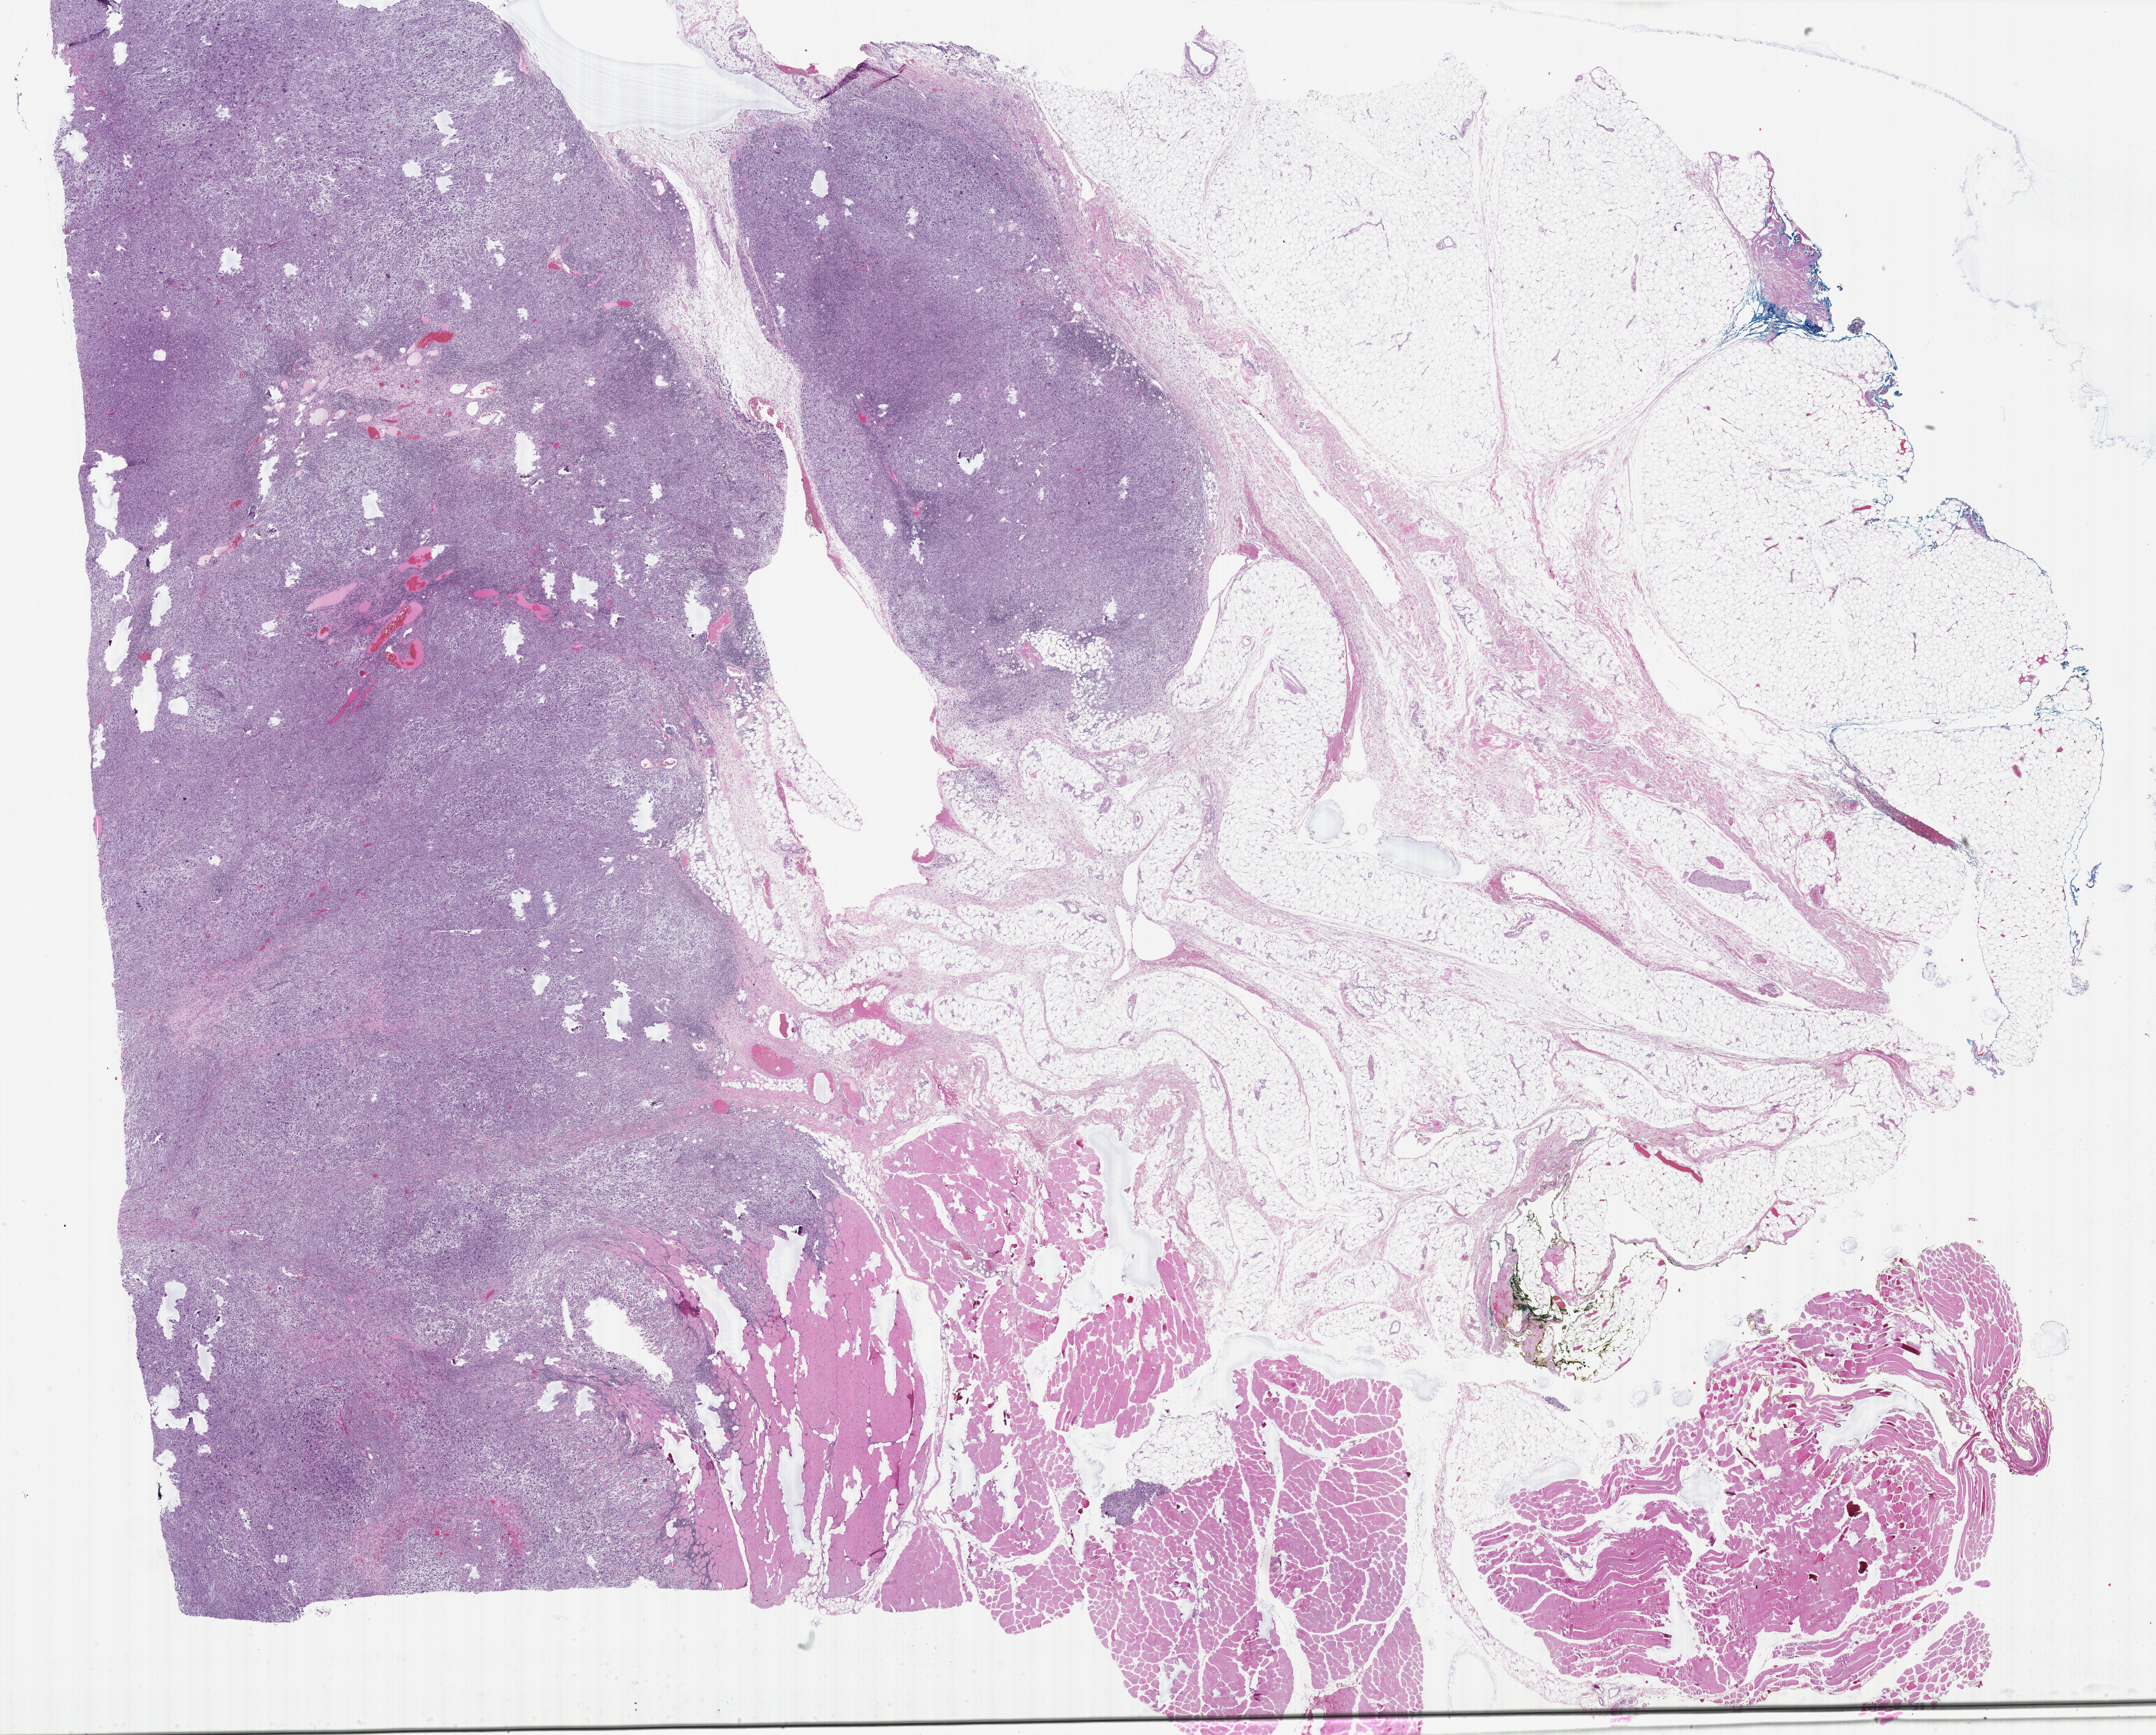
Whole-slide histology image, H&E, shown as a low-resolution overview of the whole scanned area (about 27.5 x 22.1 mm, from a 40x scan); formalin-fixed paraffin-embedded (FFPE) diagnostic section; connective, subcutaneous and other soft tissues, primary tumour sample. Male, age 86 years at initial diagnosis.
Histologic diagnosis: Undifferentiated sarcoma.